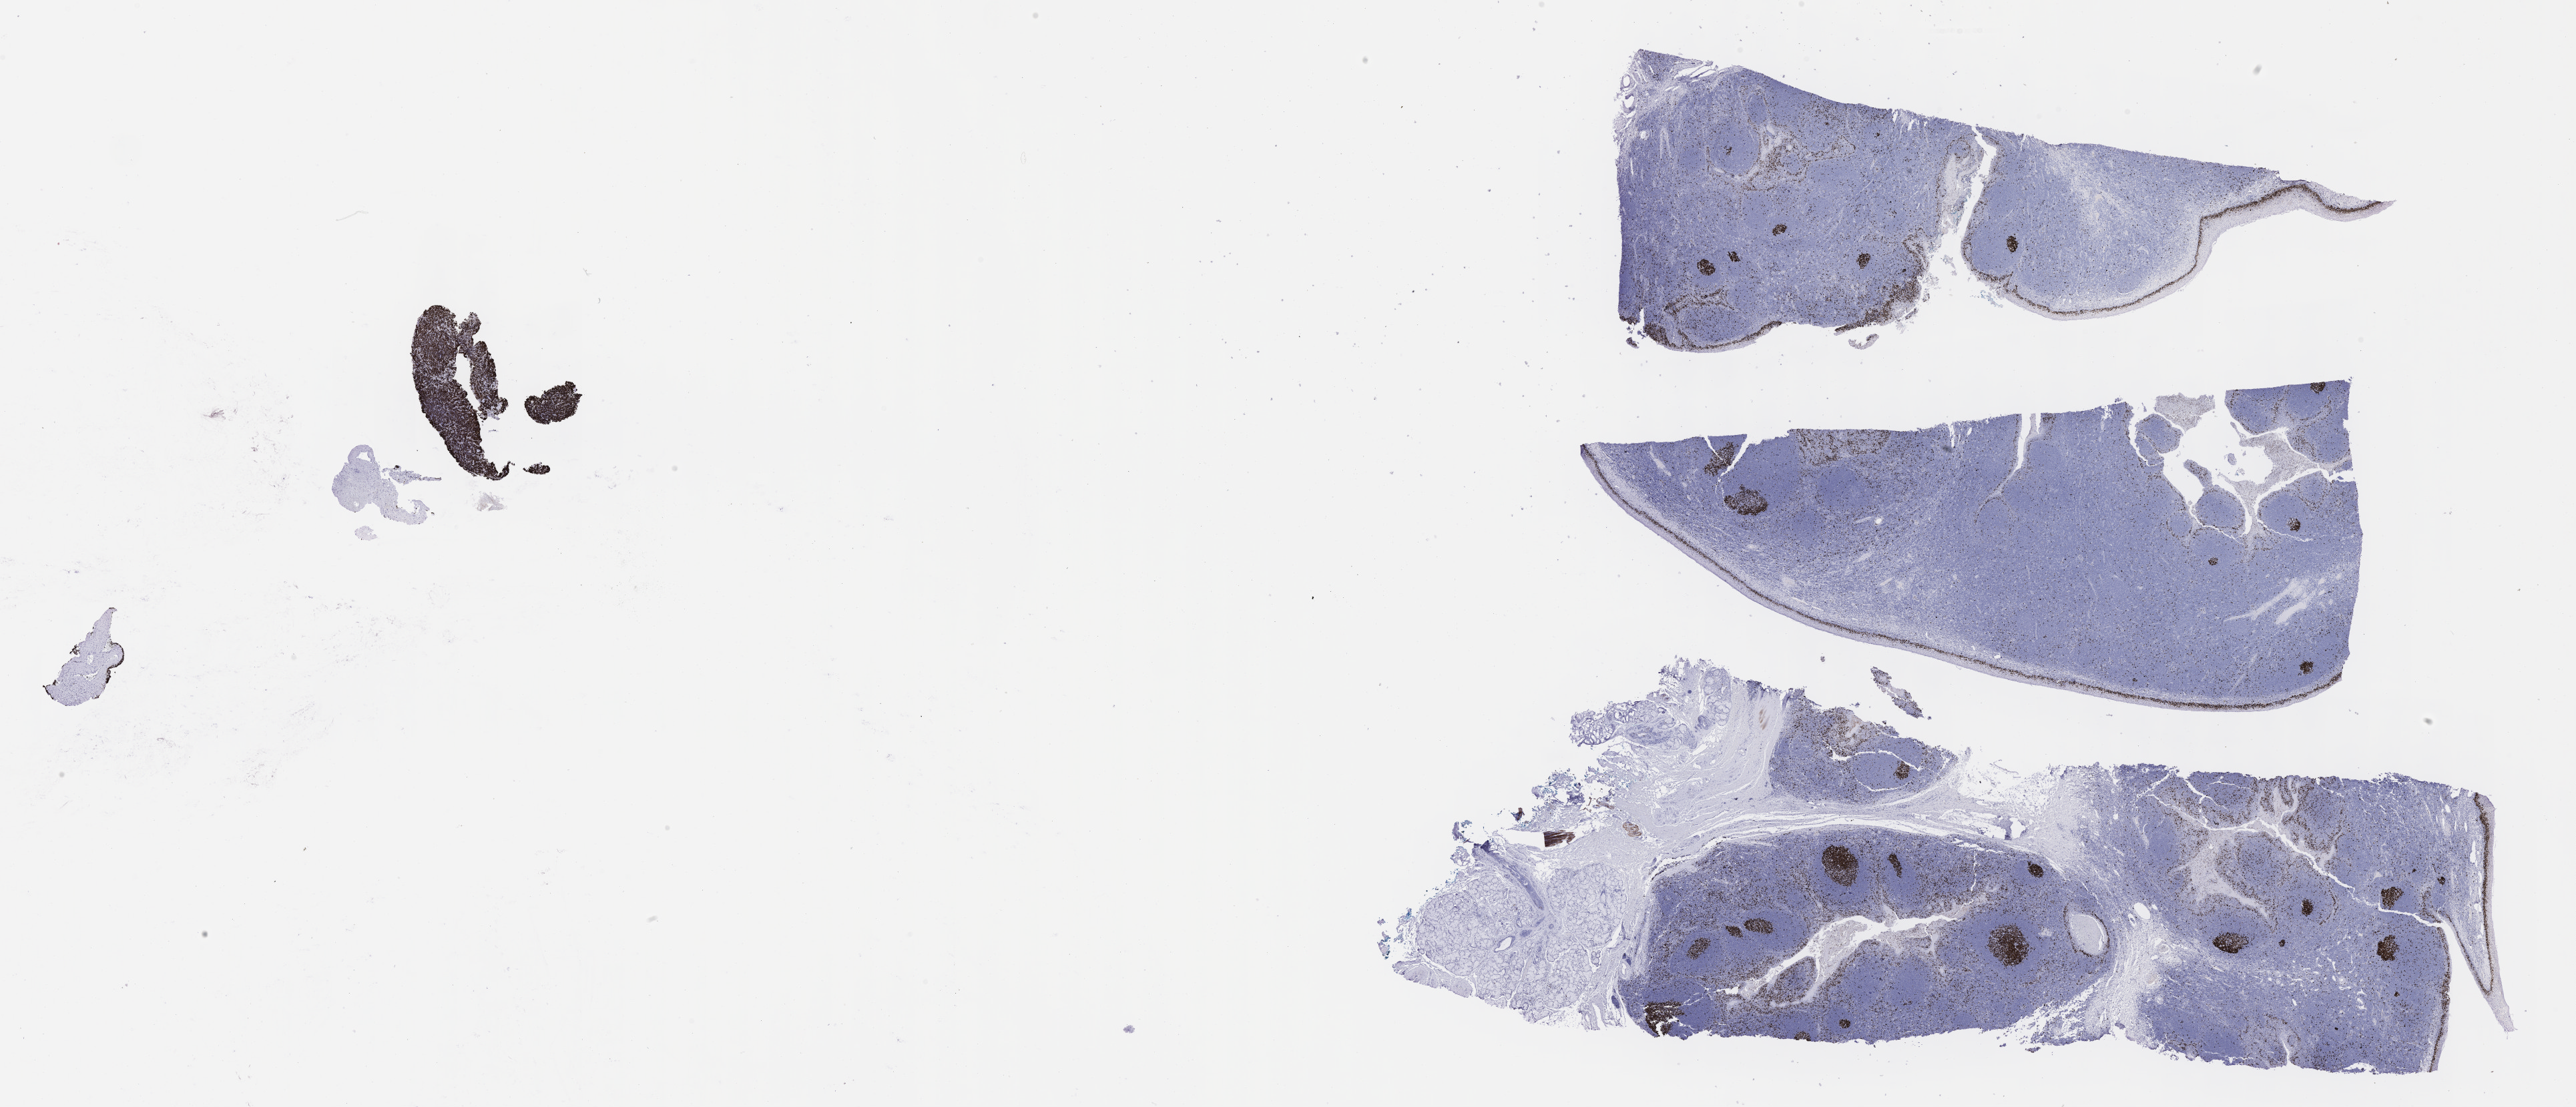
IHC for Ki-67, whole-slide image, low-resolution overview of the scanned area, about 31.2 x 13.4 mm. Tumor tissue. Anatomic site: abdomen proper. Female, age 7 years at initial diagnosis.
* diagnosis: Burkitt lymphoma, NOS